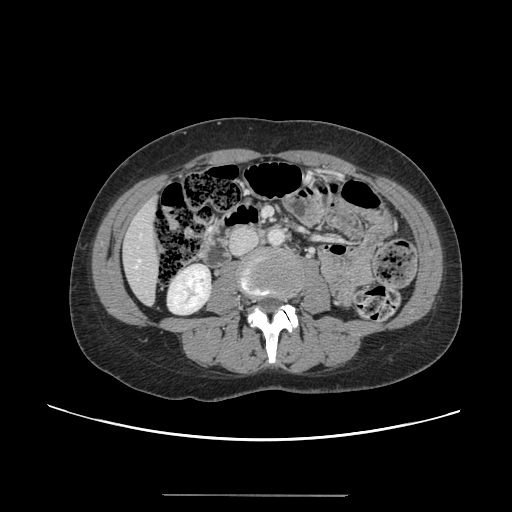
Contrast-enhanced abdominal CT, one axial slice; position 31 of 144 along the scan axis; 120 kVp; intravenous contrast given; soft-tissue window (W 400 / L 40 HU); 2.5 mm slice thickness; 512 × 512 image matrix, field of view 380 × 380 mm. Female patient, age 53 years. Case-level facts recorded for this patient, not image findings: diagnosis: colorectal cancer liver metastases, imaged before liver resection; multiple liver metastases: yes; largest metastasis: 1.1 cm.
Annotated regions visible in this slice (outlined manually by an expert reader):
- hepatic veins: bounding box <136,259,140,267> (left, top, right, bottom; pixels)
- liver: <124,203,160,302>
- planned liver remnant (the part of the liver to remain after resection): <124,202,160,303>